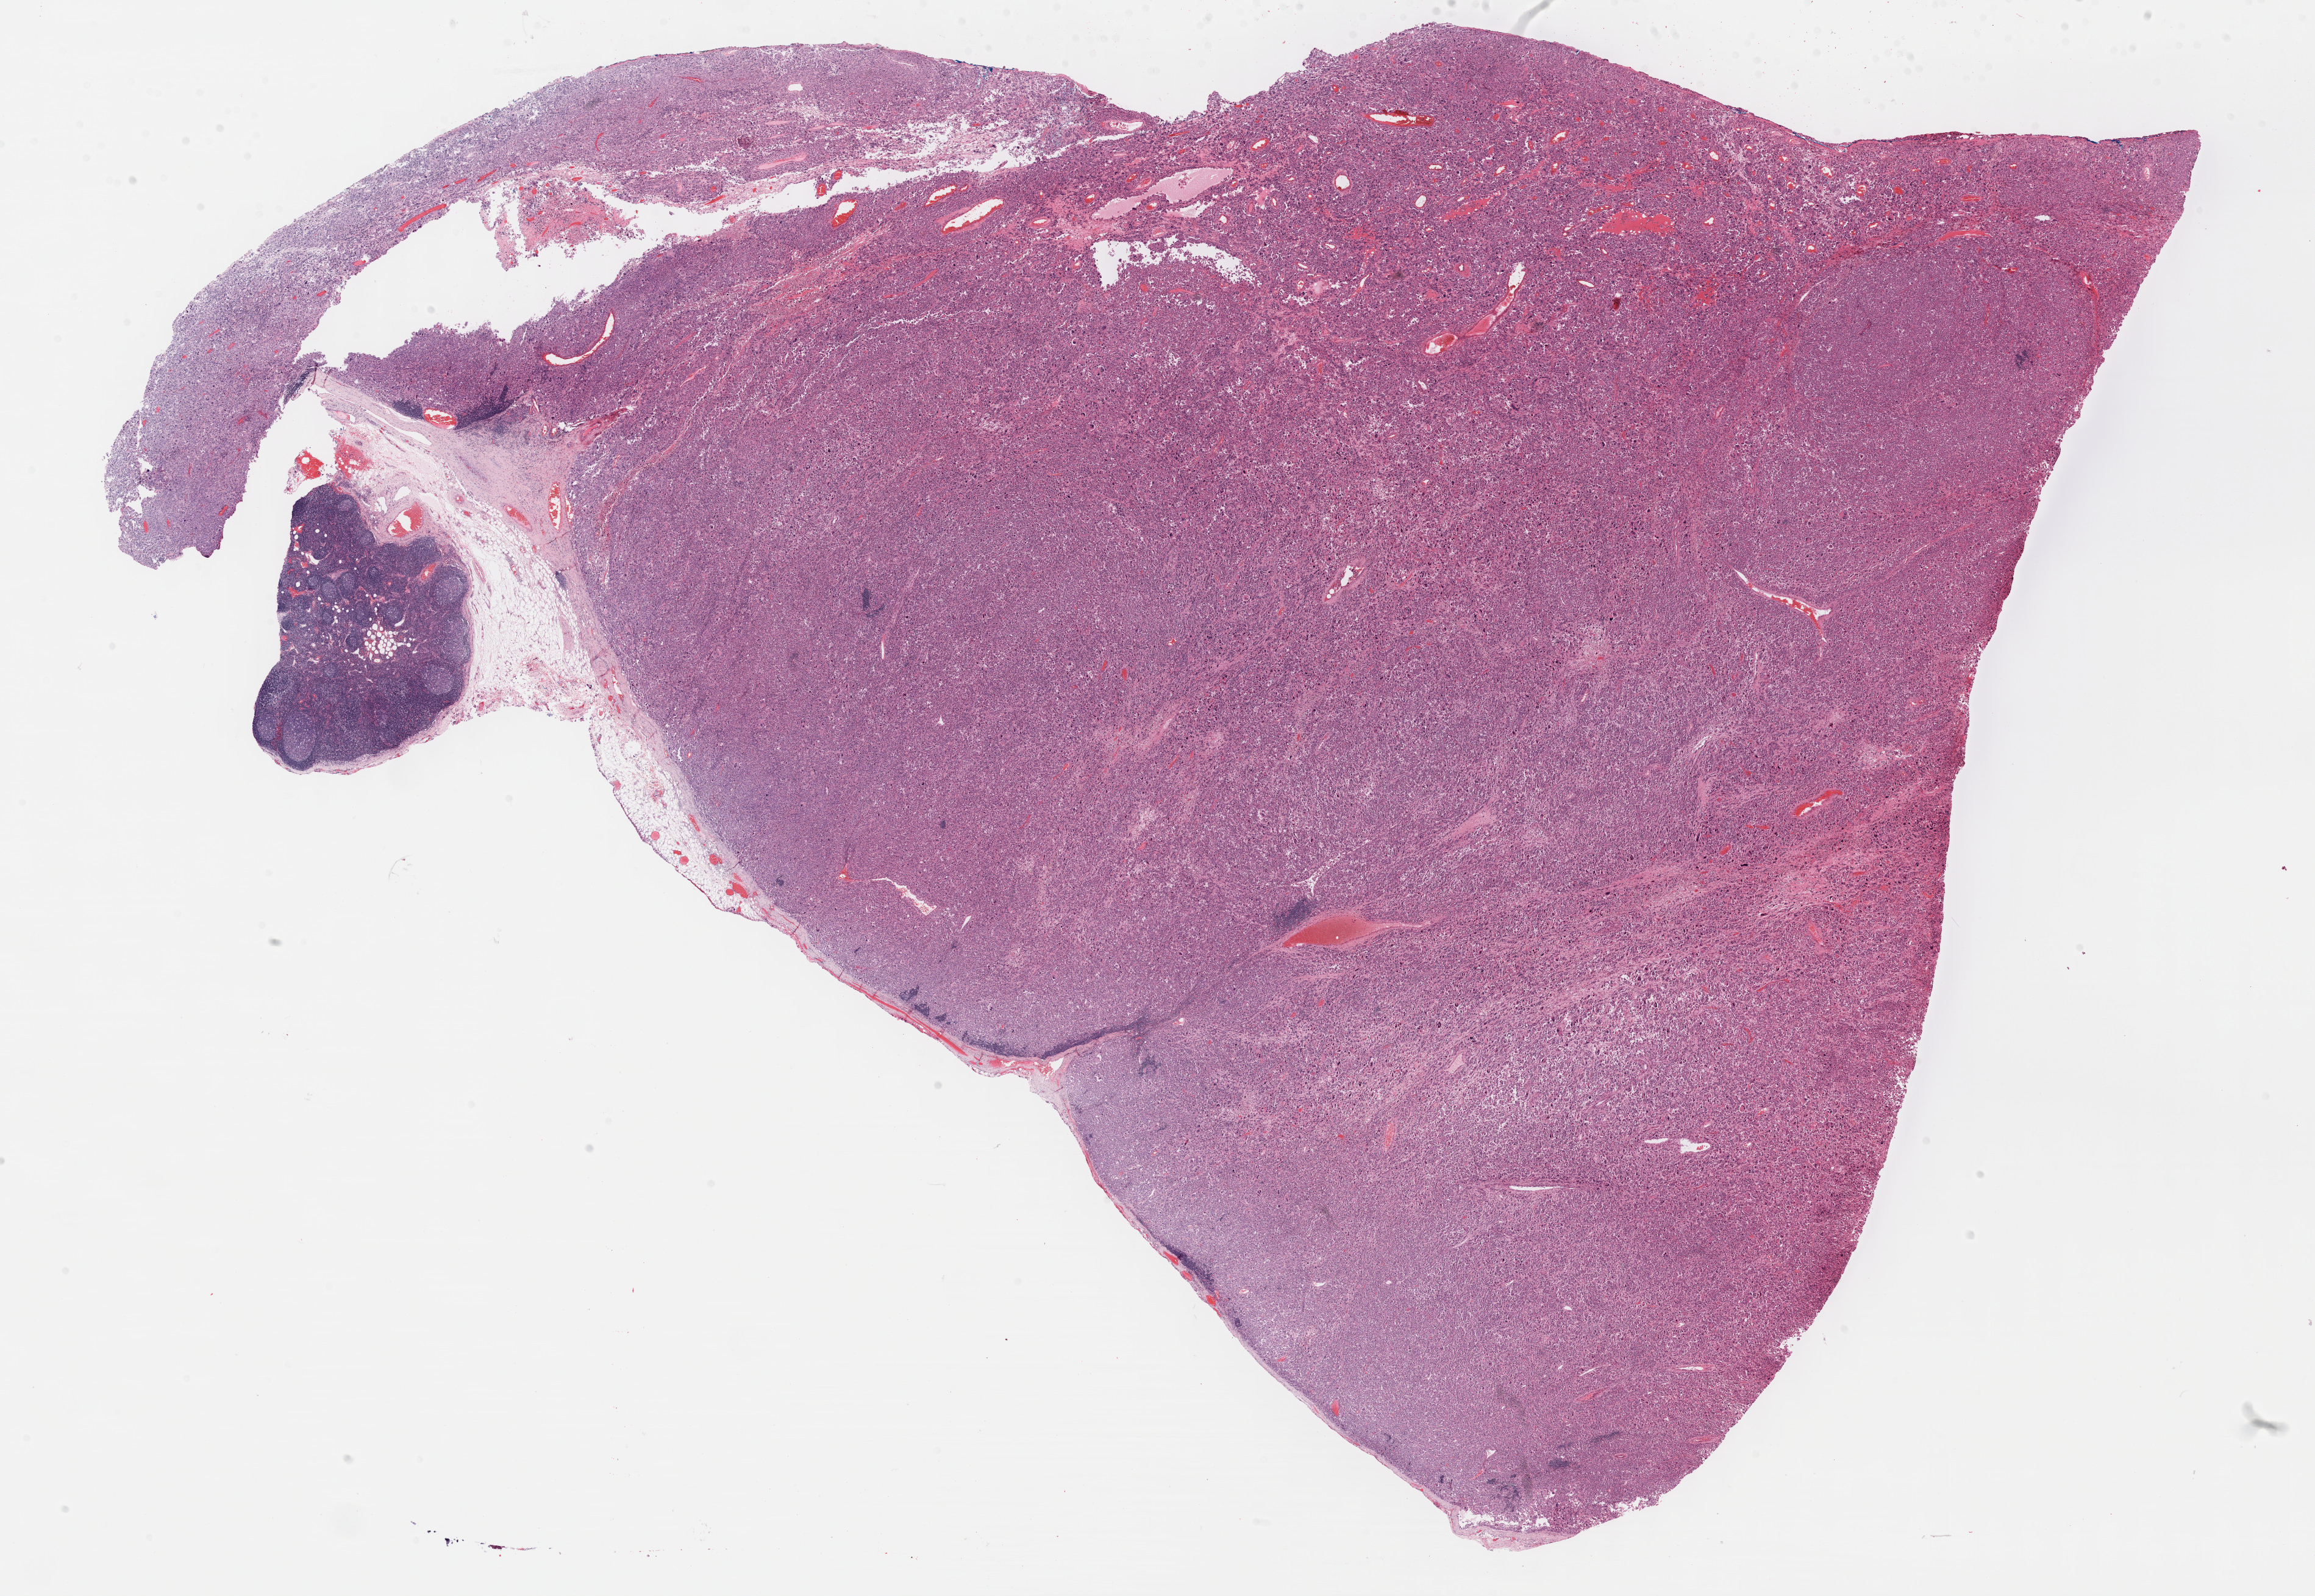
Whole-slide histology image, H&E — shown as a low-resolution overview of the whole scanned area (about 30.7 x 21.2 mm, from a 40x scan). Formalin-fixed paraffin-embedded (FFPE) diagnostic section. Metastatic tumour sample. Patient: male, age at initial diagnosis 49 years.
This section: metastatic tumour tissue. Patient diagnosis: Nodular melanoma.